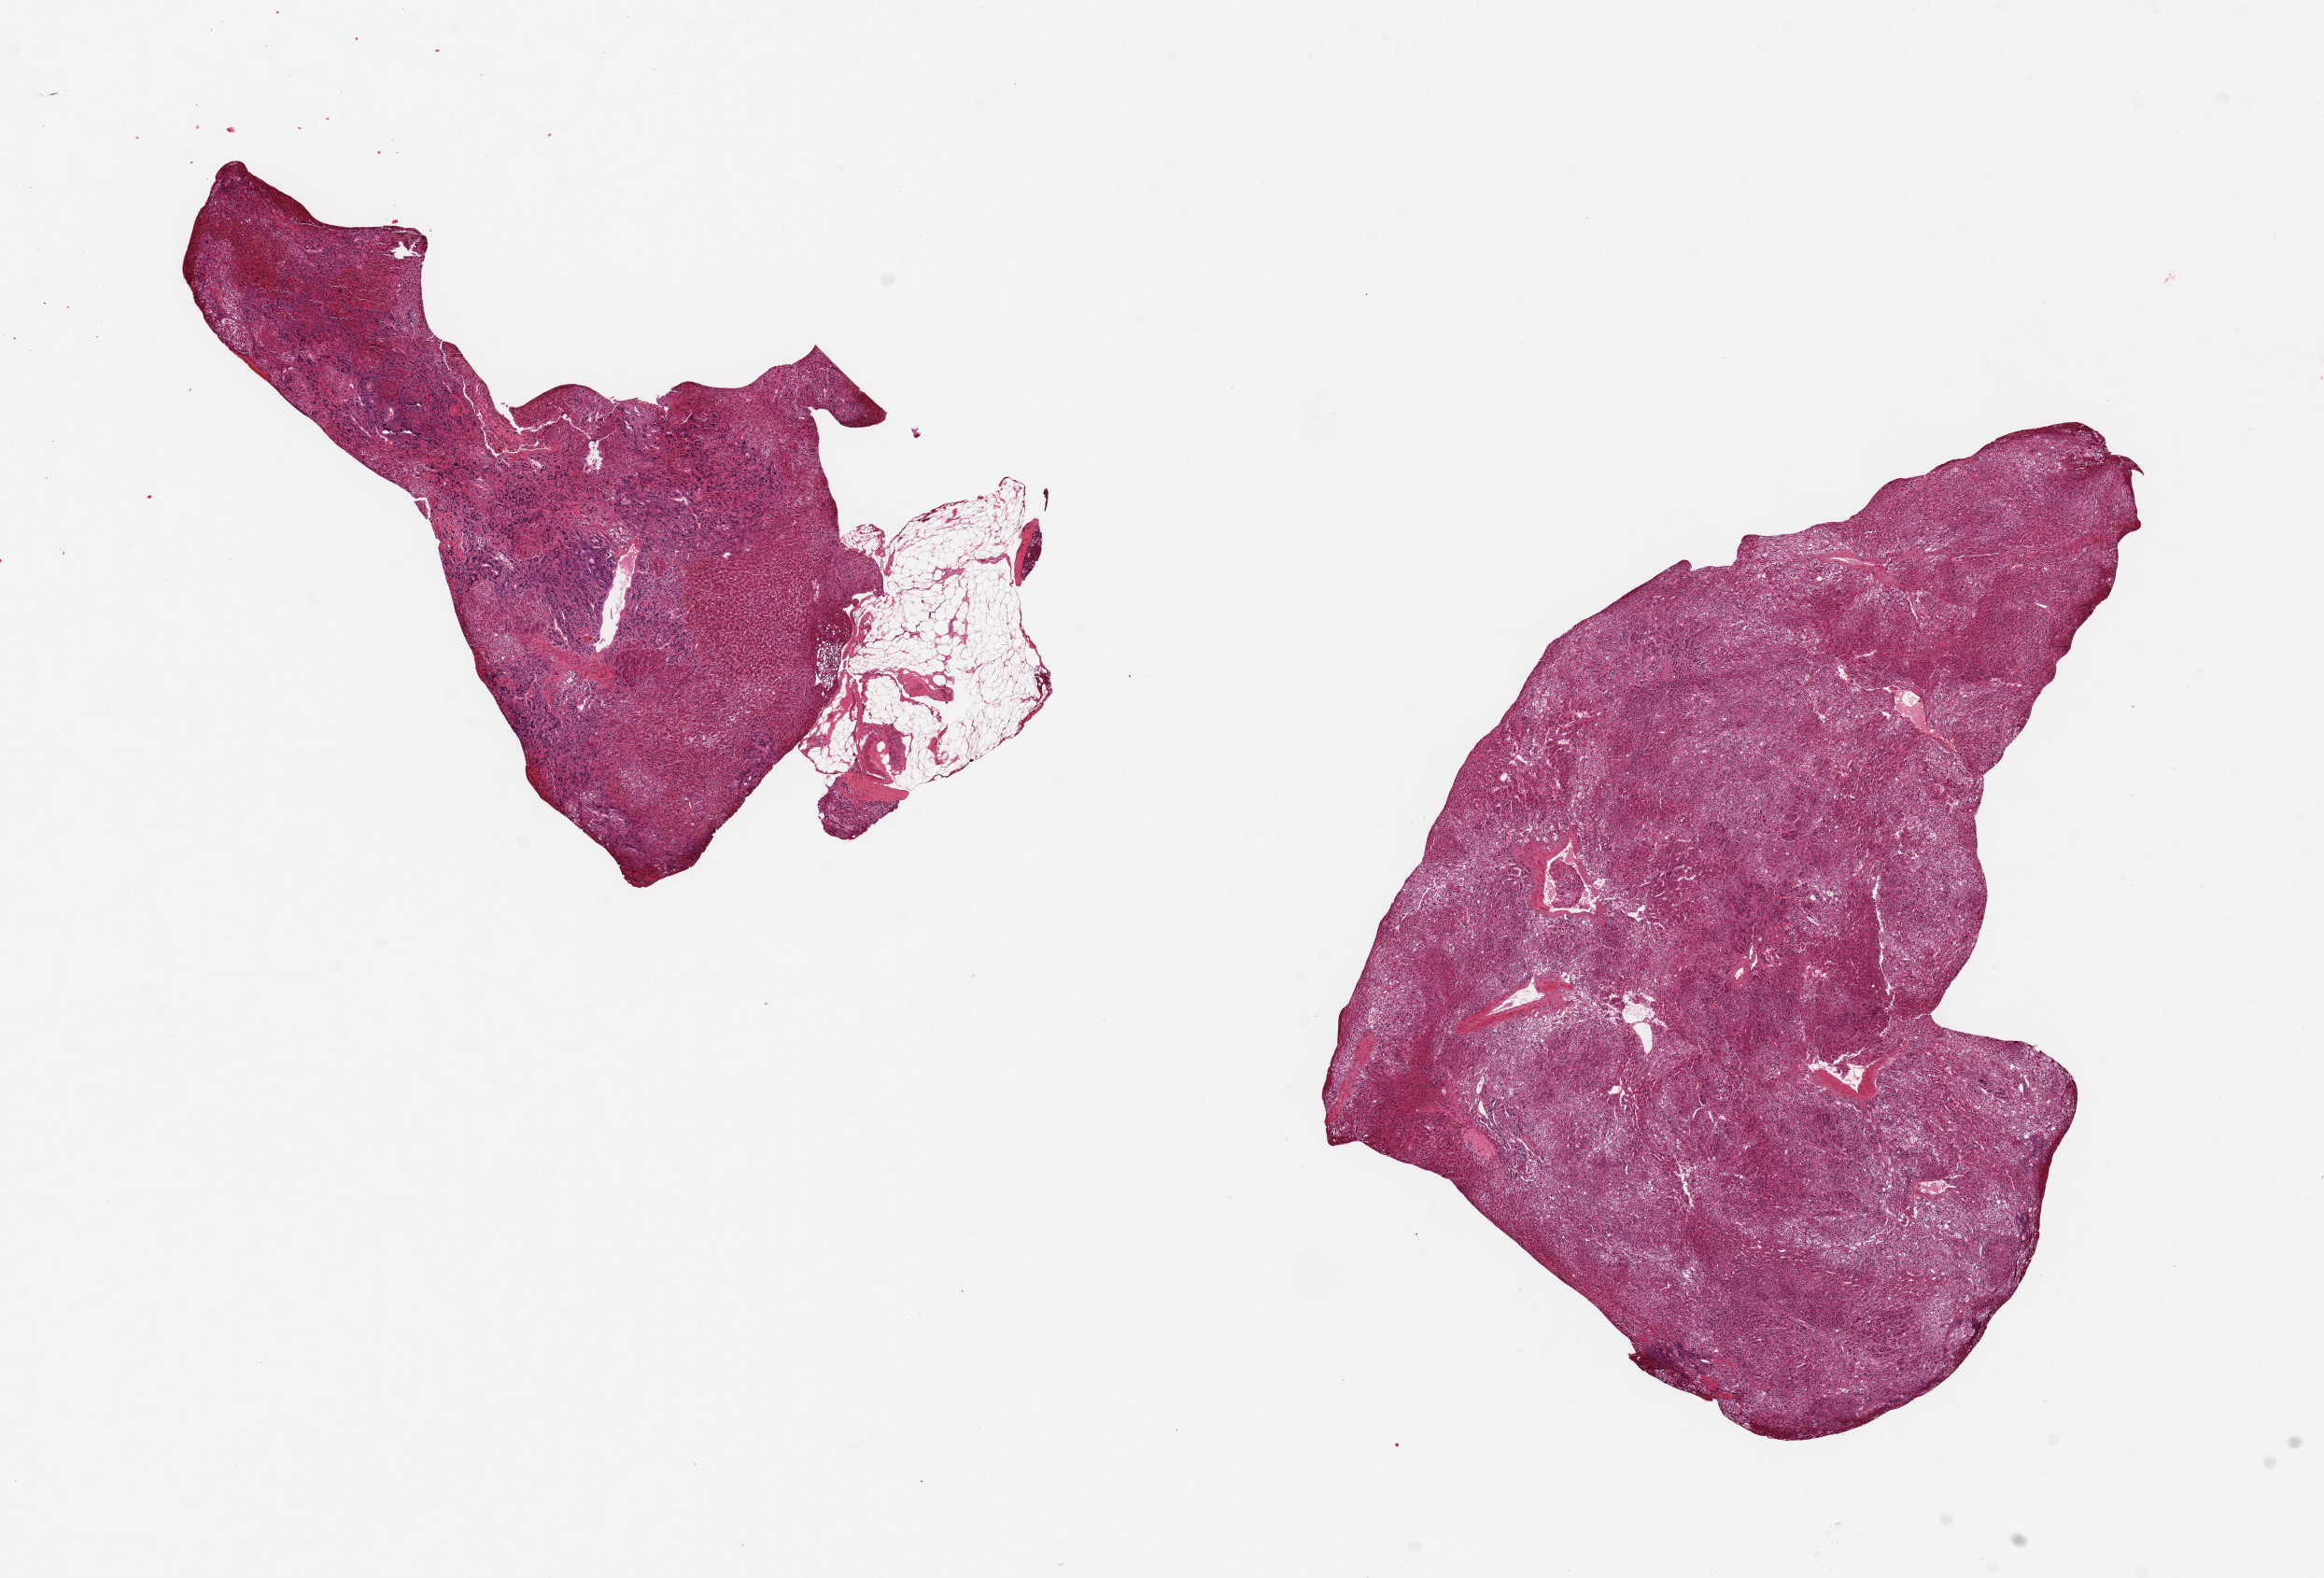
H&E whole-slide image — low-resolution overview of the scanned area, about 19.7 x 13.4 mm; PAXgene-fixed, paraffin-embedded tissue; target tissue: adrenal gland; donor tissue sample. Male donor.
Pathologist's review note for this sample: 2 pieces ~8x5mm, all cortex, one has adherent 1.5mm nubbin of fat, otherwise clean but not well preserved.